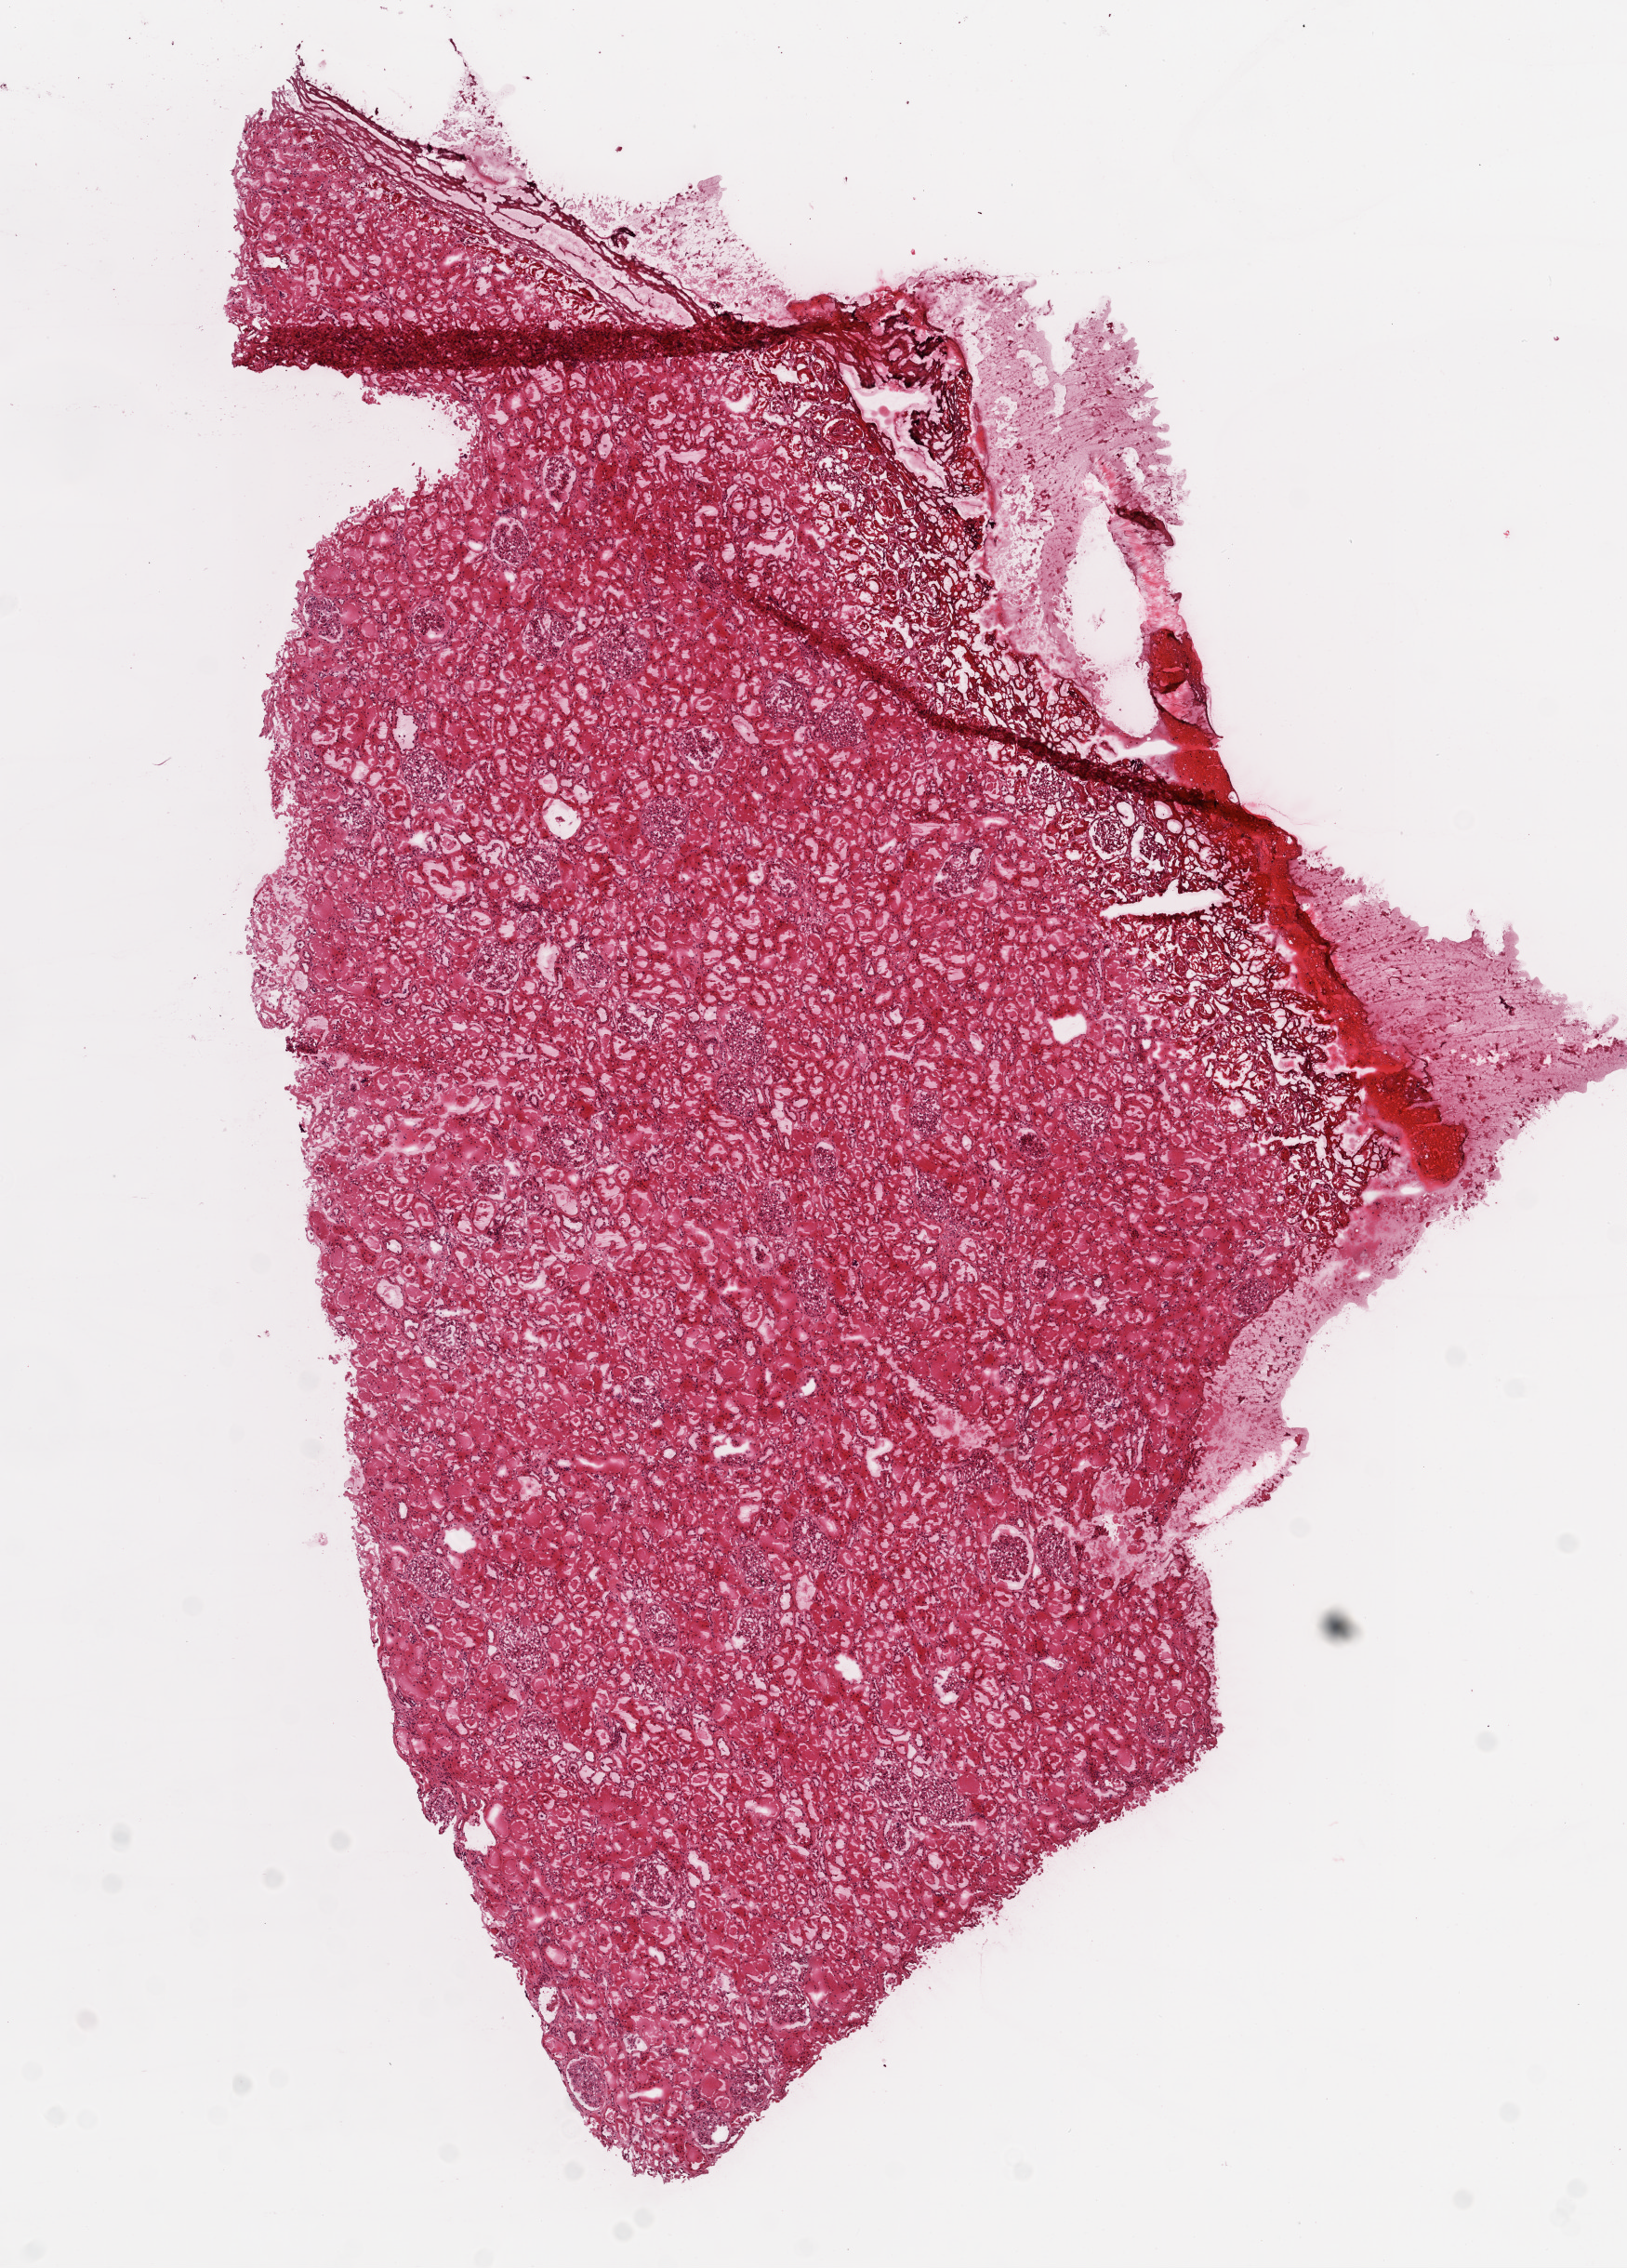
Whole-slide histology image, H&E, whole scanned area (about 7.0 x 9.8 mm) shown as a low-resolution overview. Frozen section from the top of the tissue portion. Solid tissue normal (non-tumour tissue) sample from the kidney. Male patient; age at initial diagnosis 57 years.
This section: solid tissue normal sample (biorepository sample class). Patient diagnosis: Clear cell adenocarcinoma, NOS.